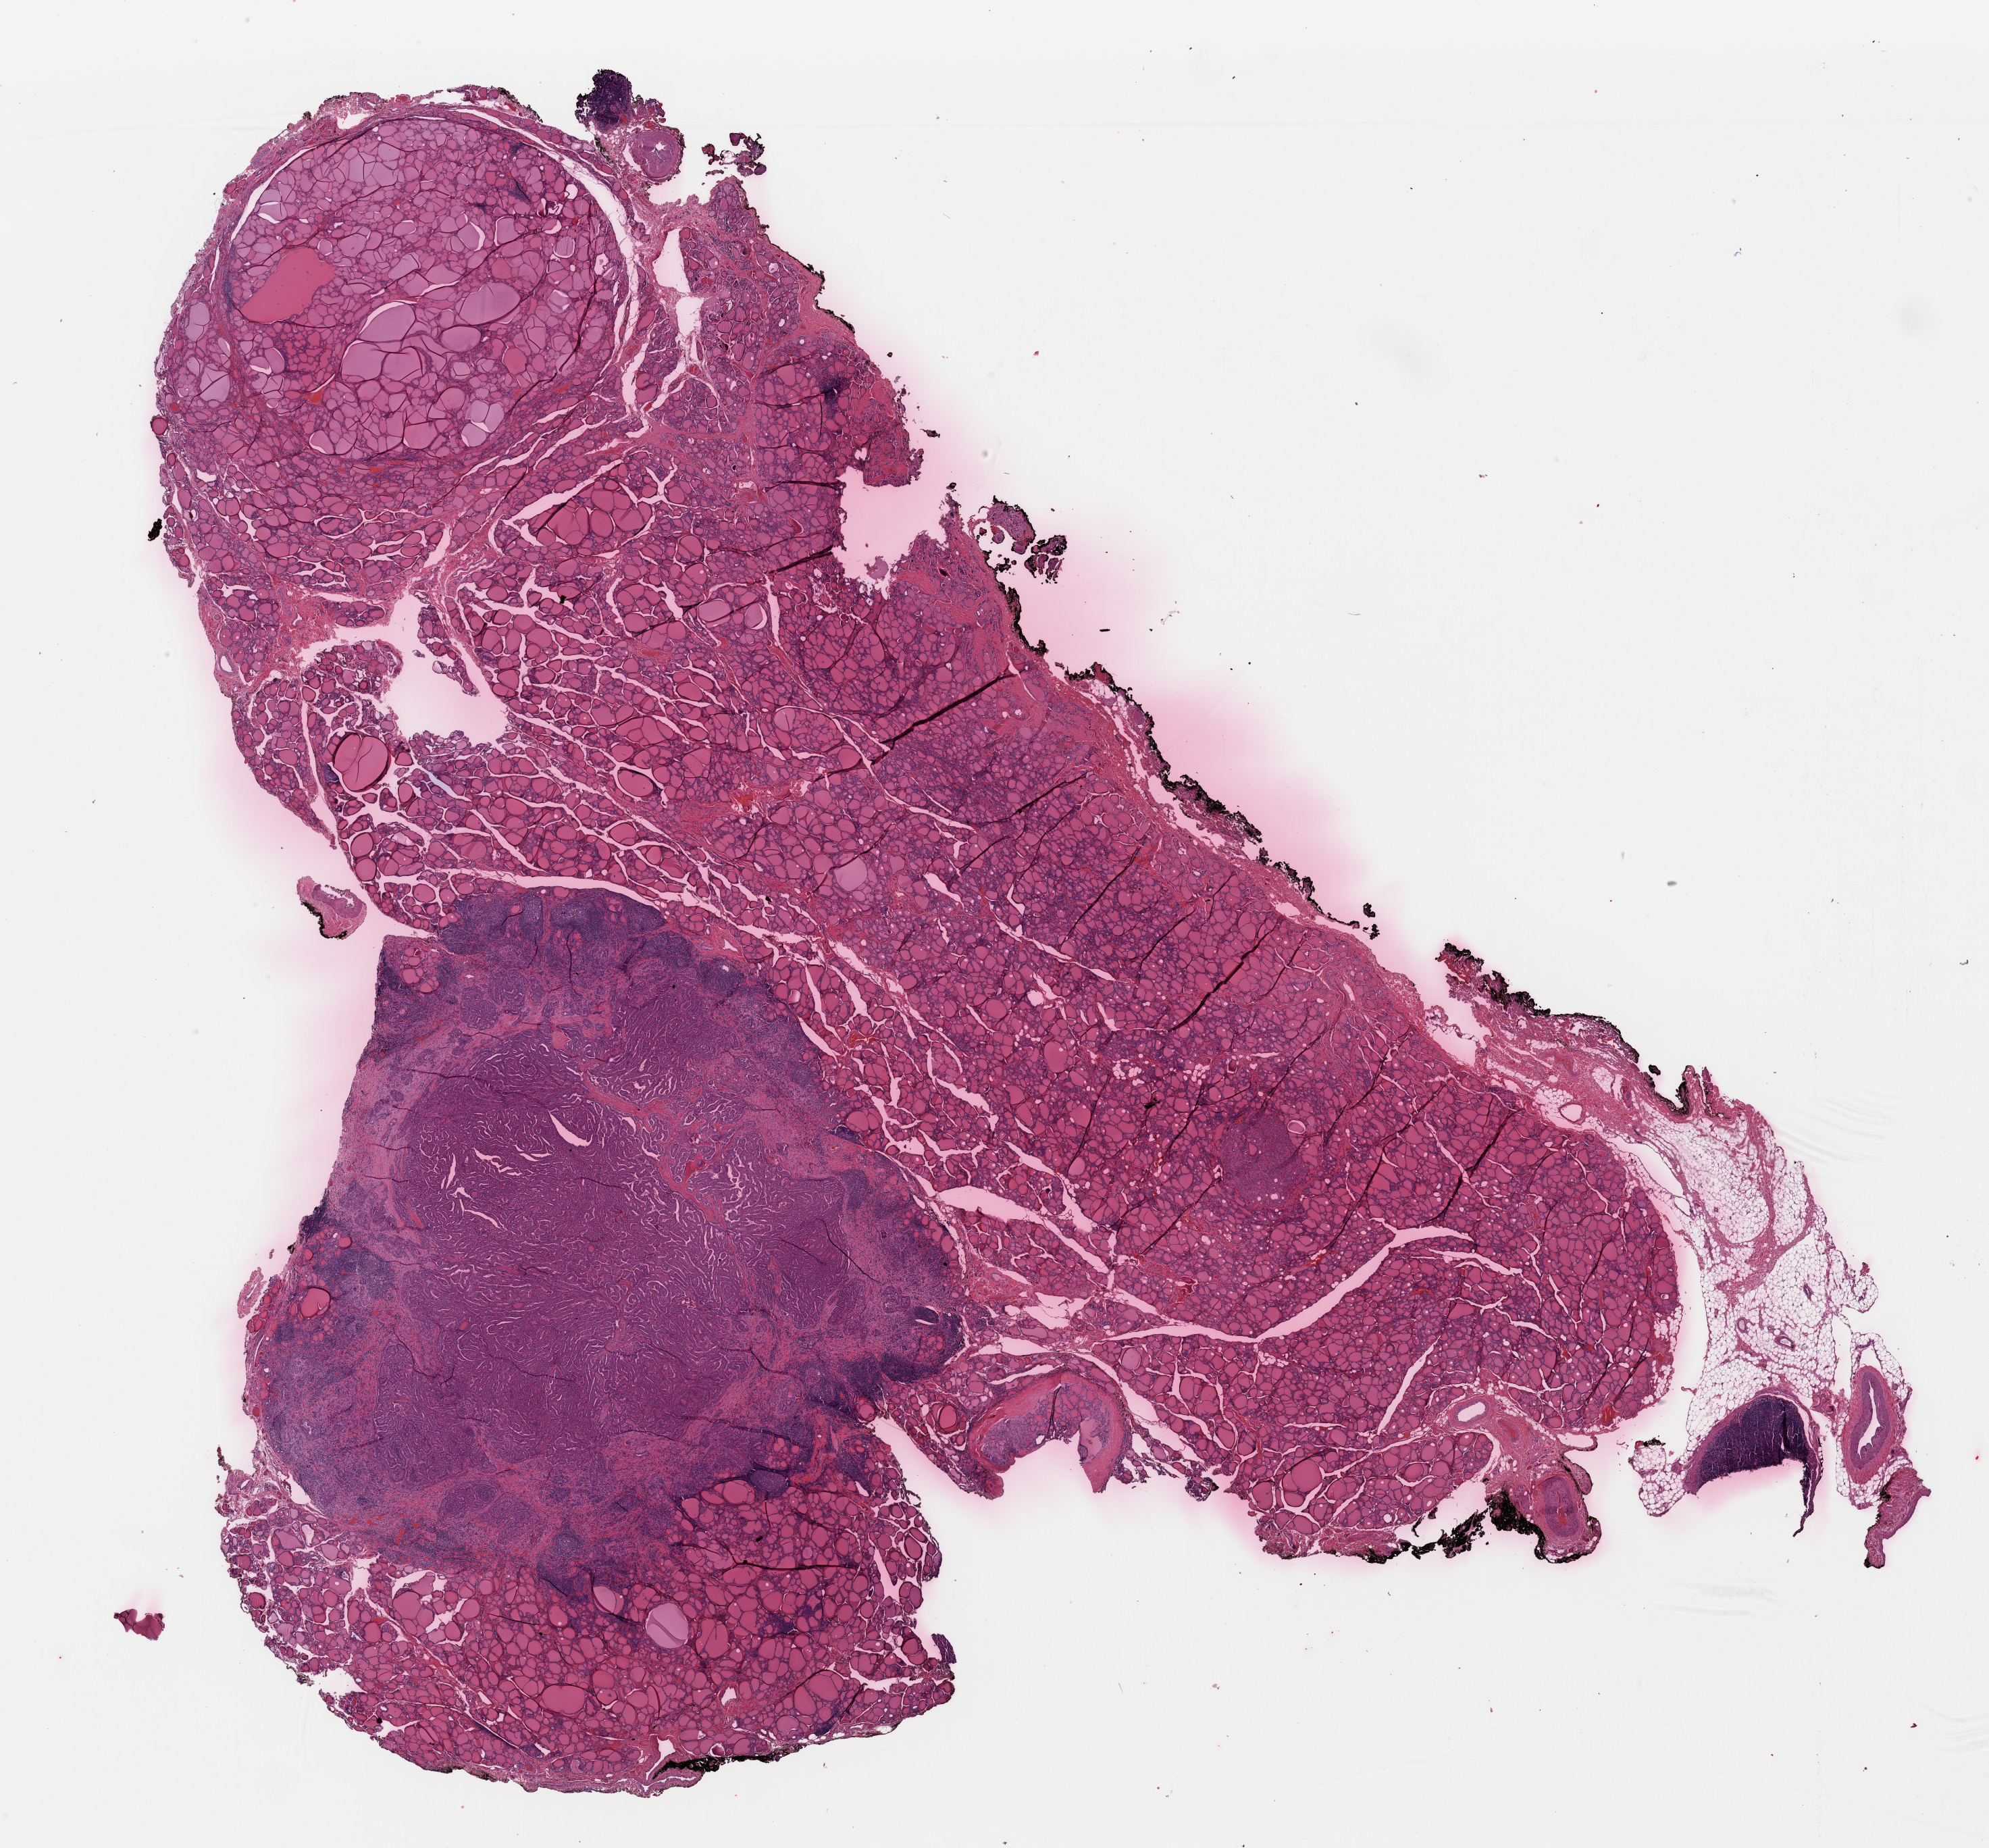
Hematoxylin and eosin (H&E) stained whole-slide image, low-resolution overview of the scanned area, about 23.3 x 21.6 mm (from a 40x scan), FFPE section, thyroid, primary tumour sample. Female, age 55 years at initial diagnosis.
- histologic diagnosis: Papillary carcinoma, columnar cell
- lymph nodes positive (case pathology): 0 of 8 examined
- laterality: bilateral
- AJCC pathologic stage: I (7th edition)